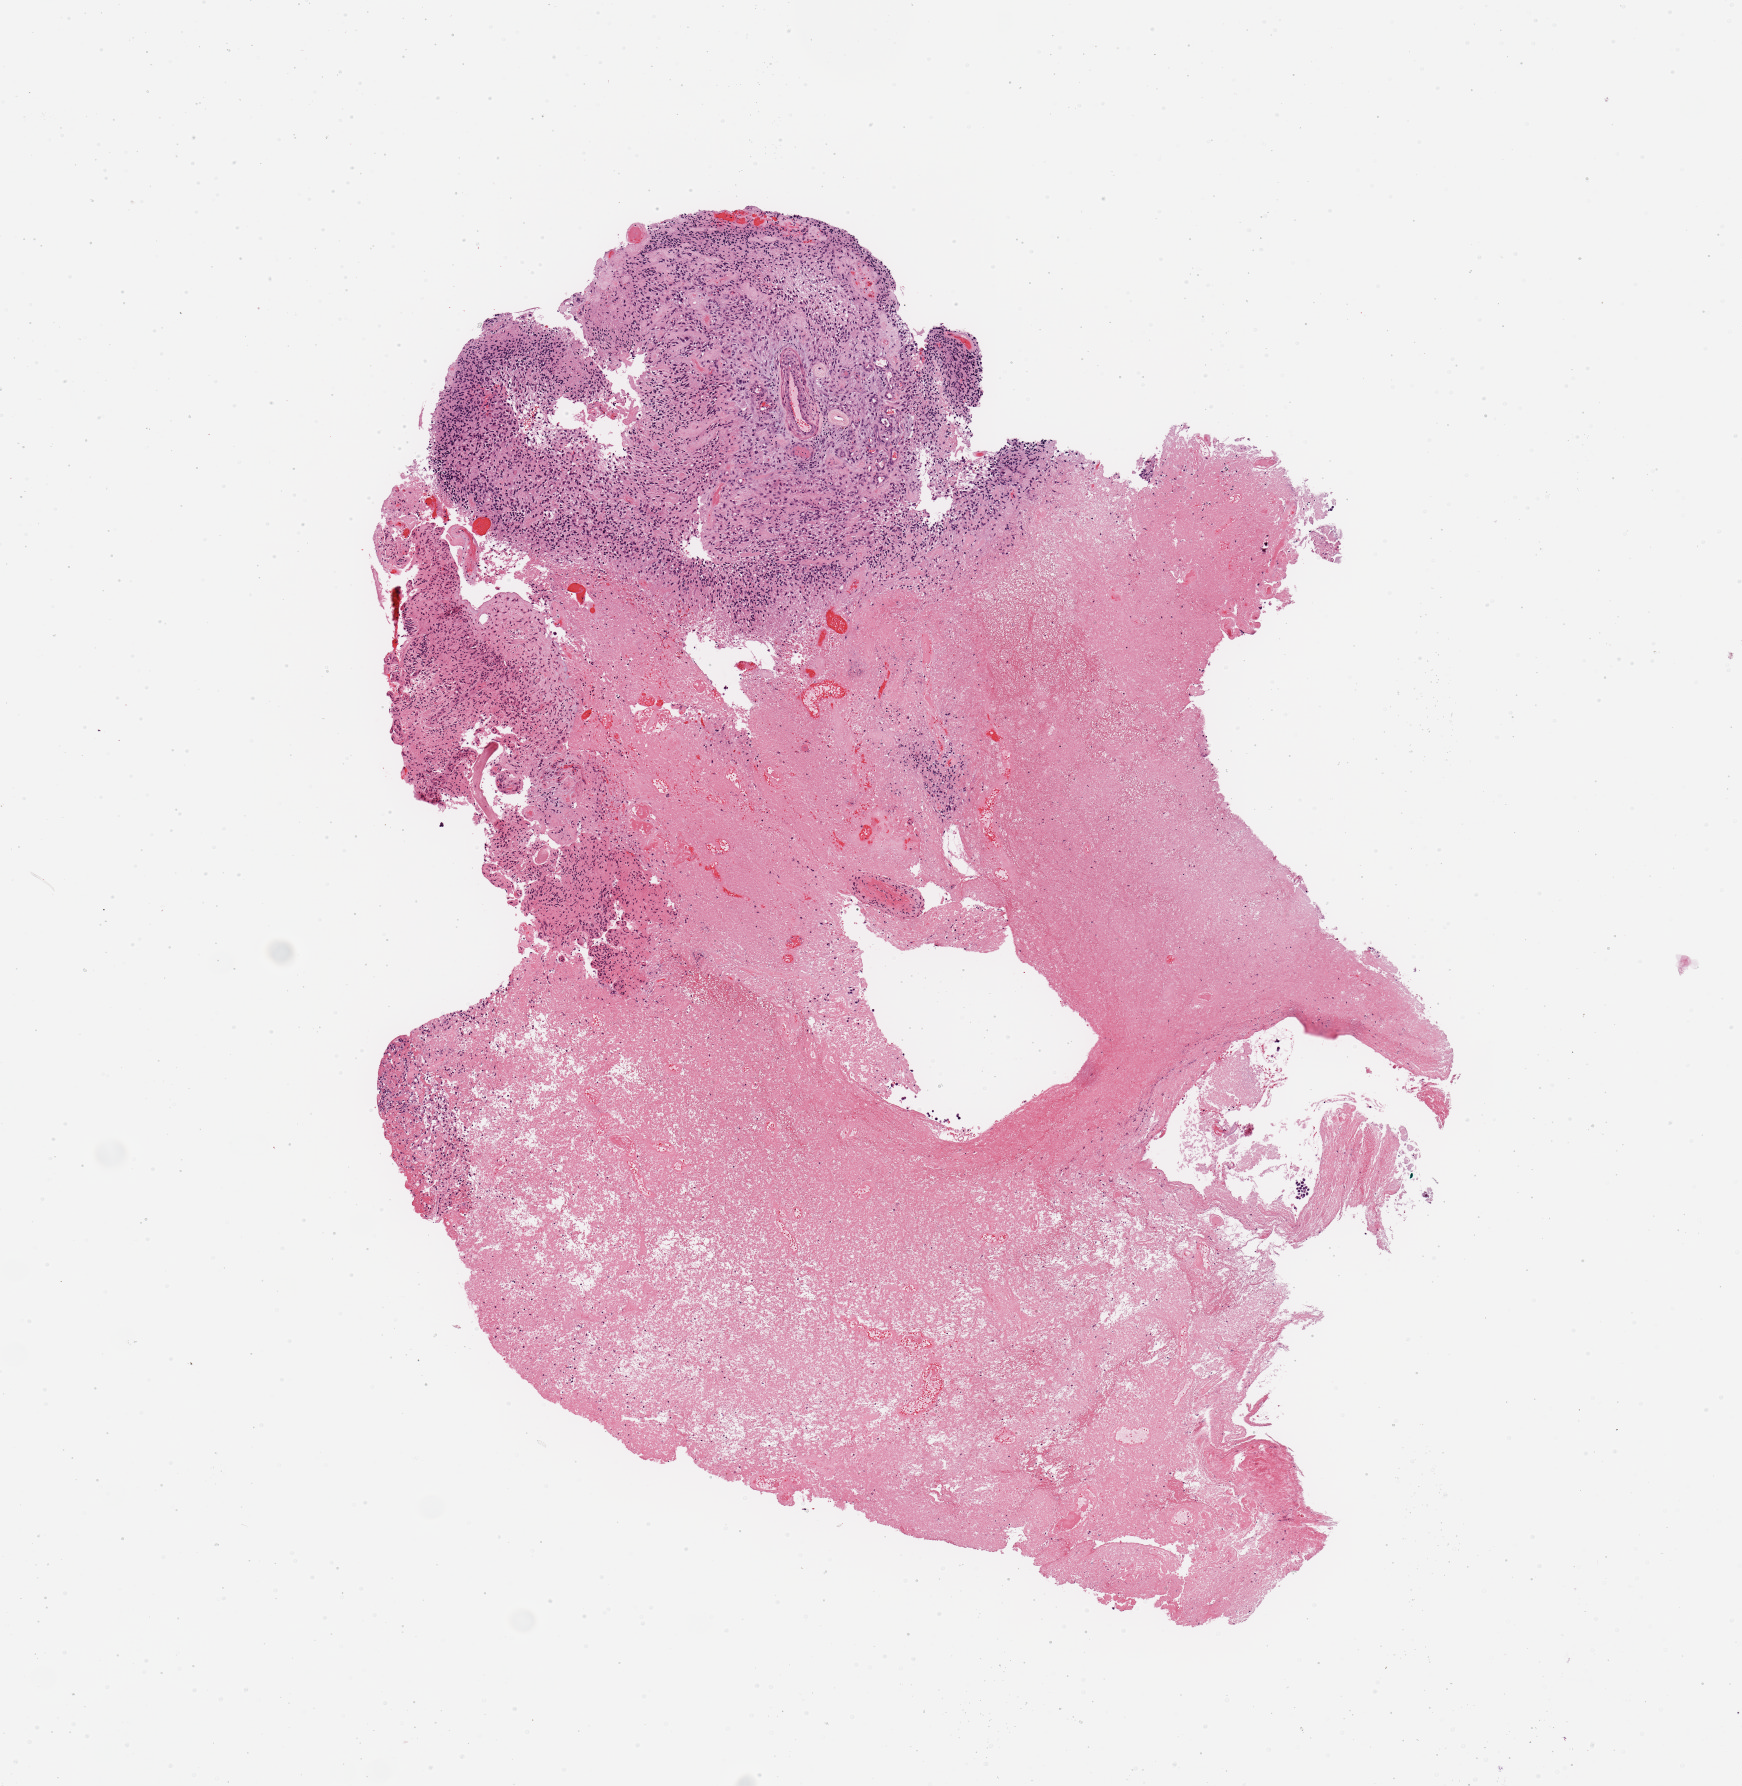
Digitized H&E tissue section (whole slide) — shown as a low-resolution overview of the whole scanned area (about 6.9 x 7.1 mm). Tumour tissue sample, sampled site: brain. 59-year-old female patient. Composition of this section per pathologist review: tumour nuclei 70%, necrosis 20%.
Diagnosis: Glioblastoma.